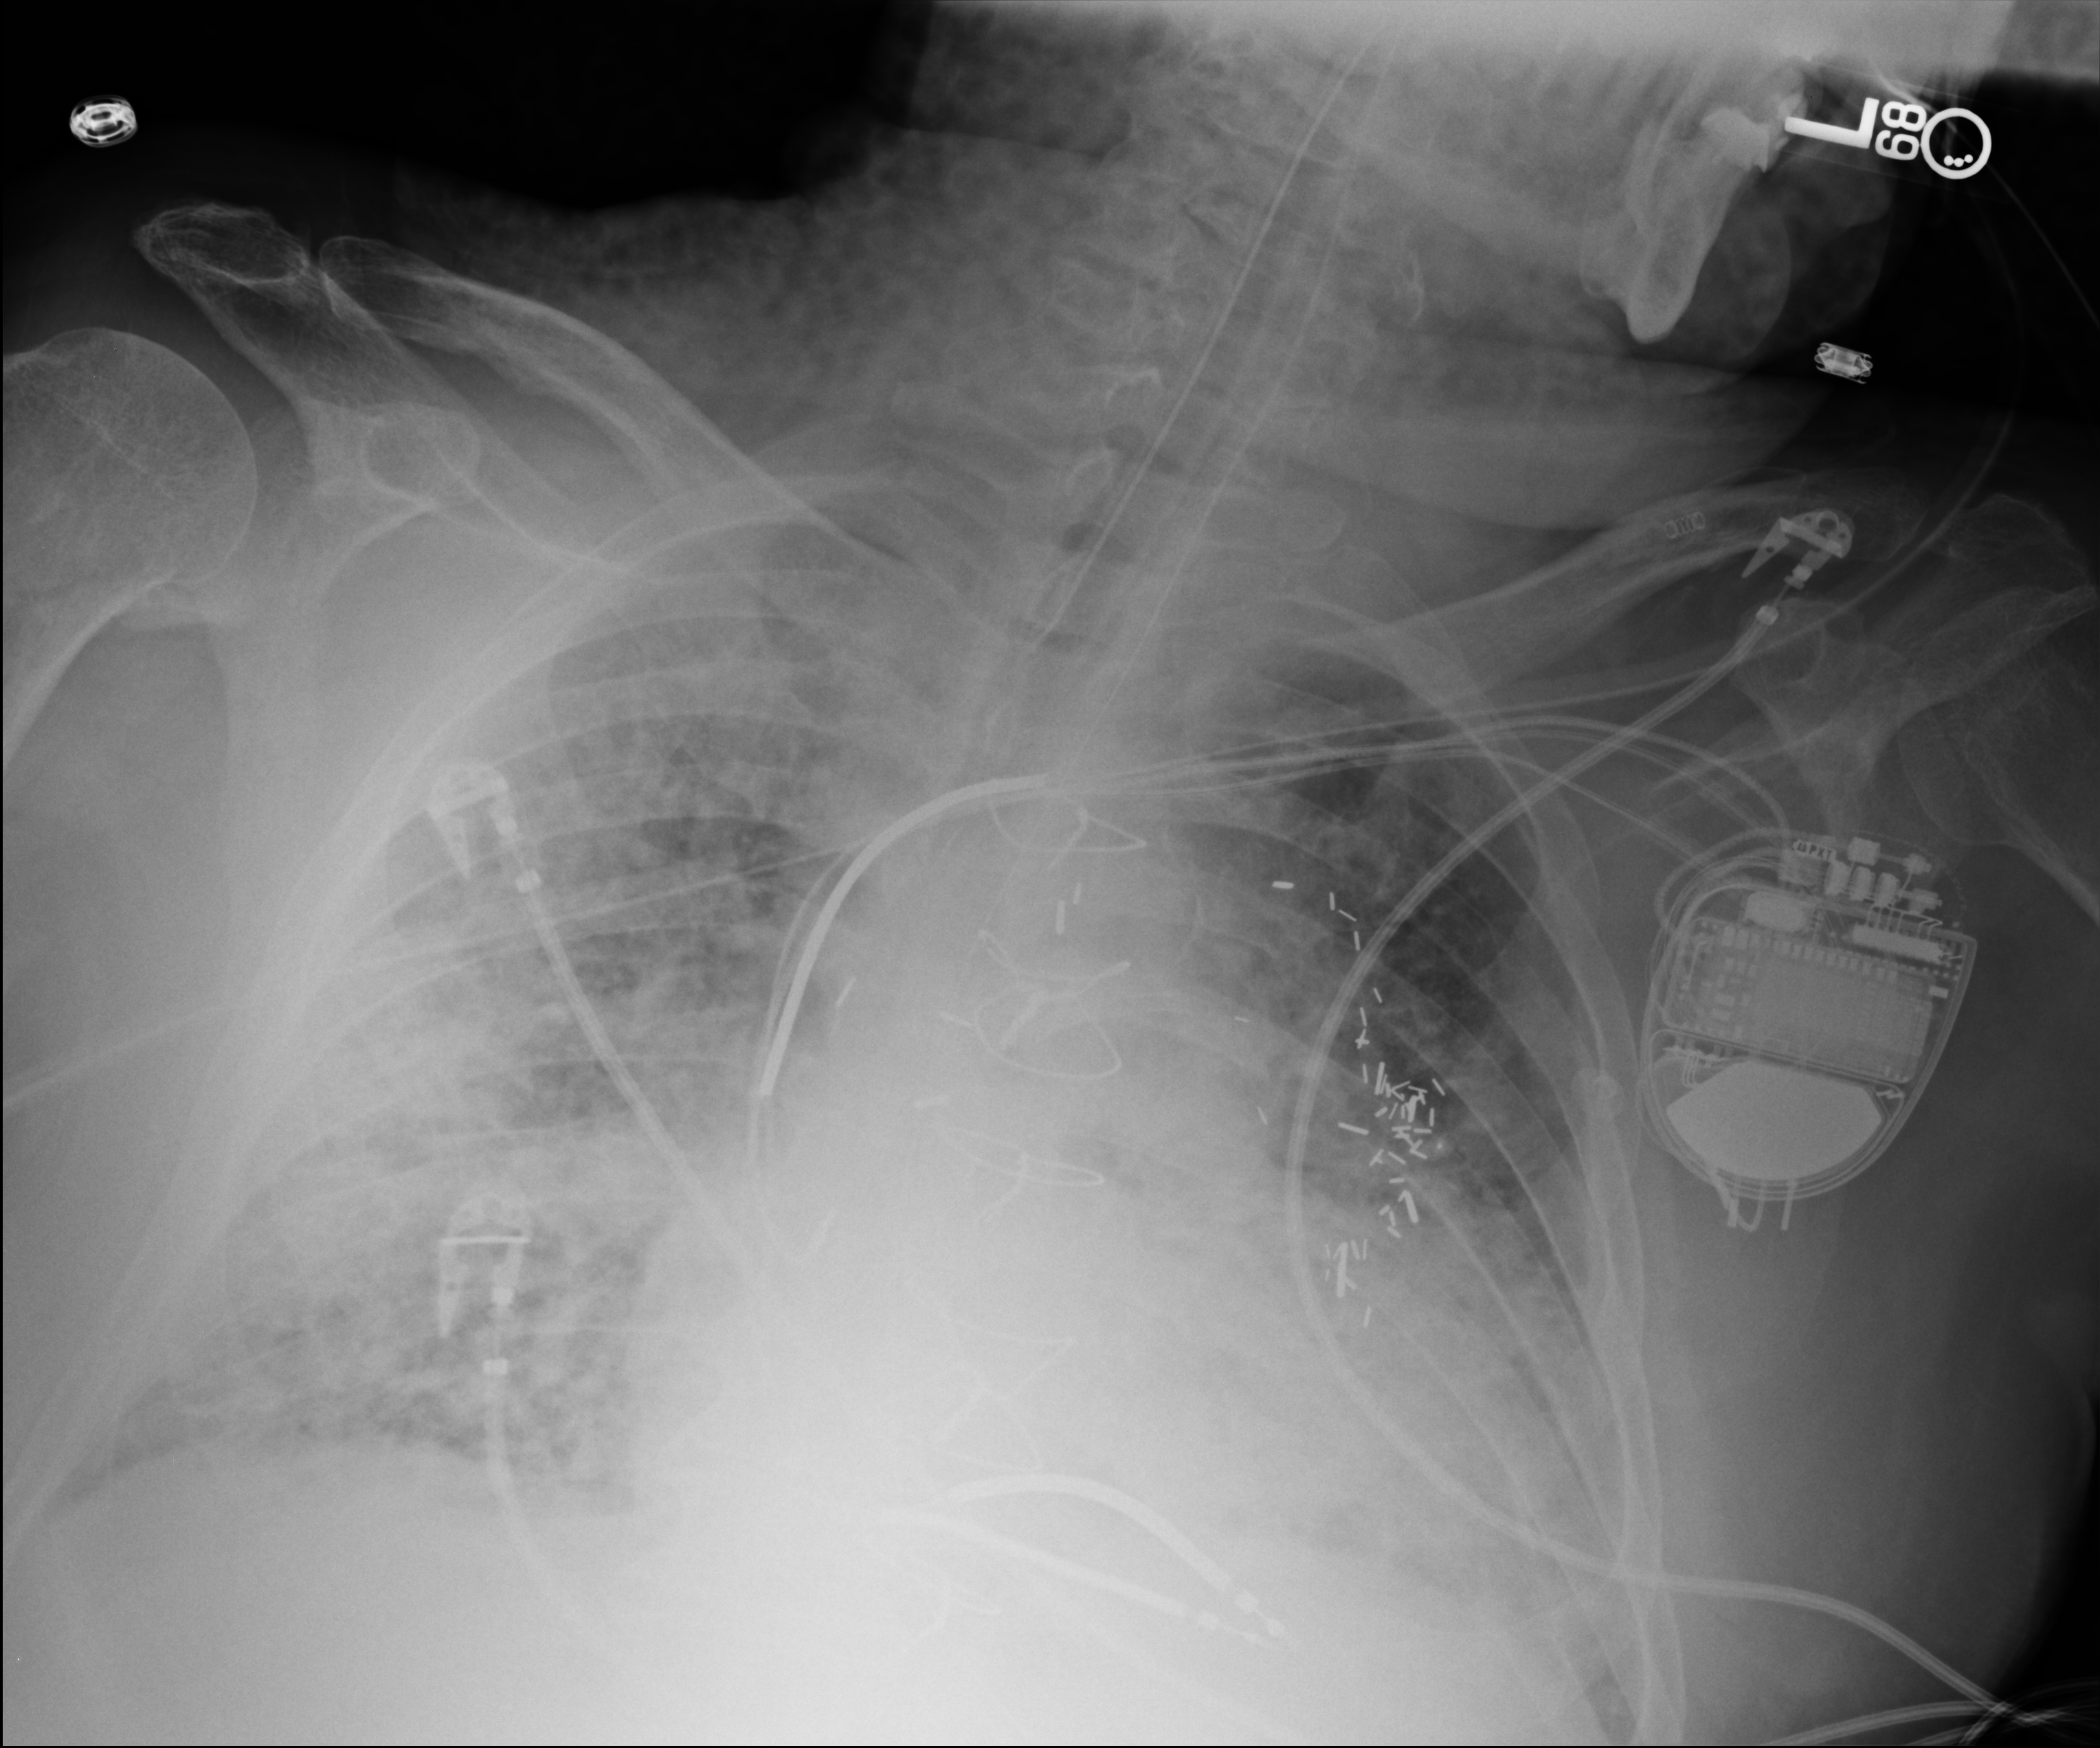
Portable chest radiograph; anteroposterior (AP) projection. Male patient hospitalised with COVID-19, age 60–74 years.
Hospital-stay facts (about this admission, not read from this image; timing relative to this image not recorded):
- diabetes (admission record): yes